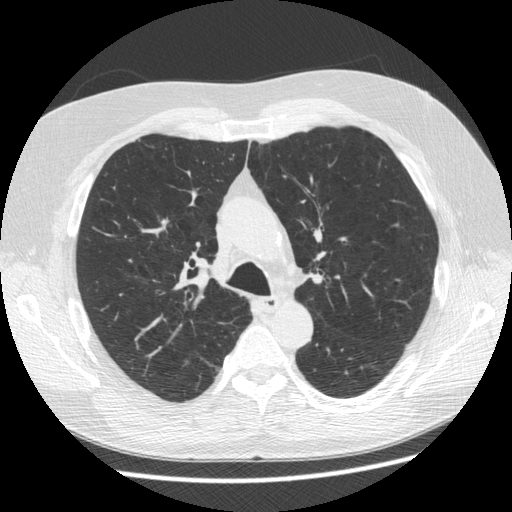
Low-dose screening chest CT, axial slice; third annual screen; lung window (W 1500 / L -600 HU); 1.25 mm slice thickness; standard (soft-tissue) reconstruction kernel (STANDARD); 120 kVp; slice 168 of 545 in the series. Male participant, aged 63 years at enrolment. Former smoker at enrolment.
Lesion marked by an expert reader, bounding box <150,210,182,239> (left, top, right, bottom; pixels). The screening reader recorded 2 non-calcified nodules or masses ≥4 mm on this exam (right upper lobe, left upper lobe); which of them this box marks is not recorded.